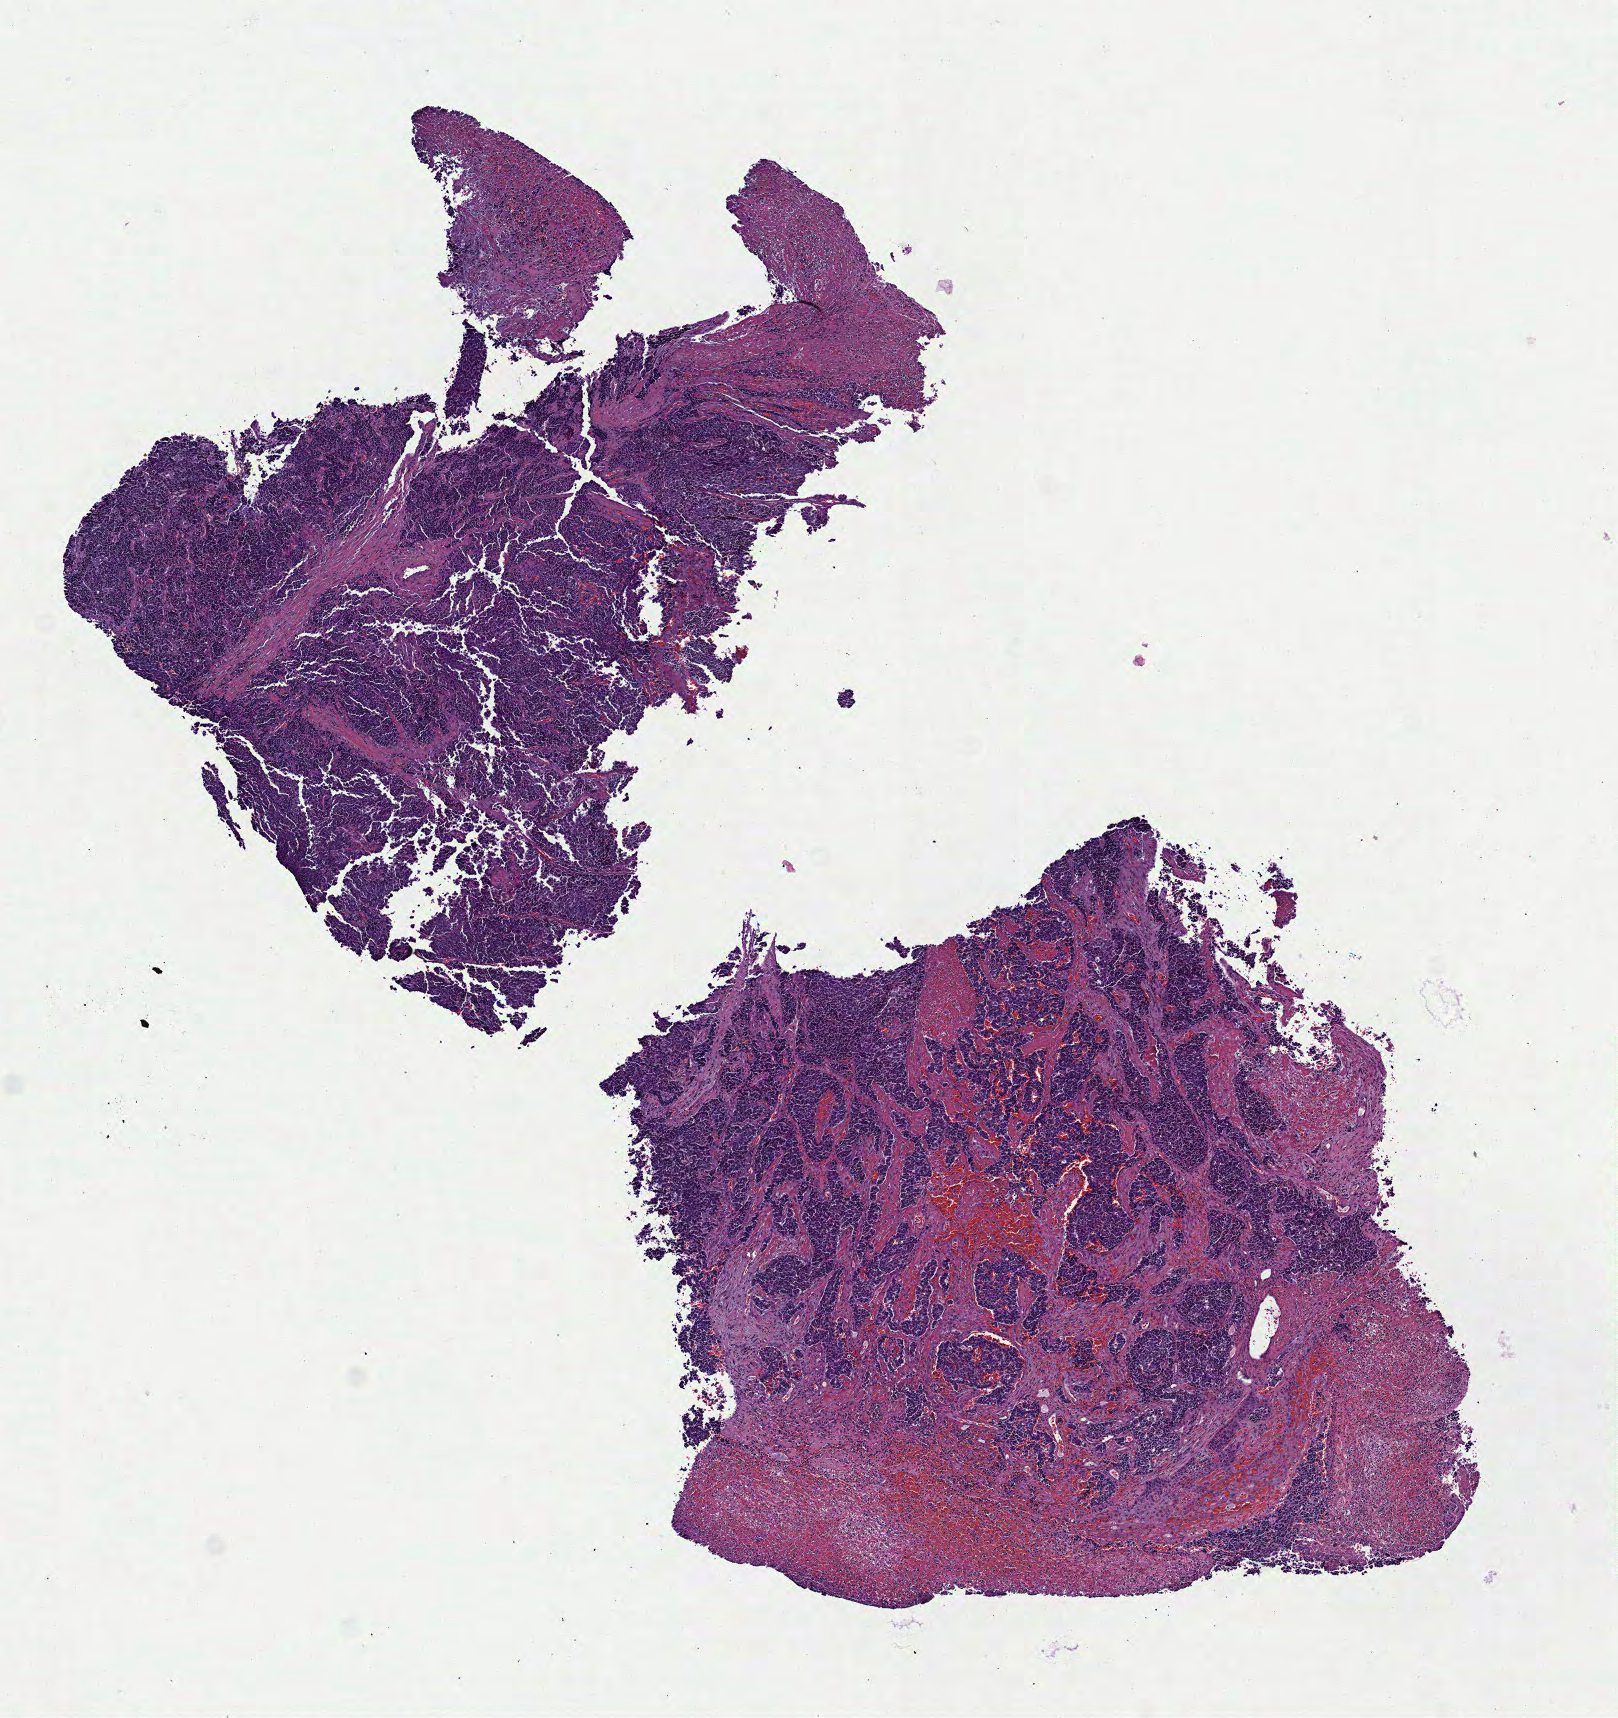
Whole-slide histology image, H&E-stained — low-resolution overview of the scanned area, about 6.5 x 6.9 mm (slide scanned at 40x); FFPE section; primary tumour sample from the head and neck. Male patient; age at initial diagnosis 56 years. Histologic grade: G3 (poorly differentiated).
- TNM: T3 N2b MX
- AJCC pathologic stage: IVA (7th edition)
- diagnosis: Squamous cell carcinoma, NOS (tonsil, NOS)
- laterality: left